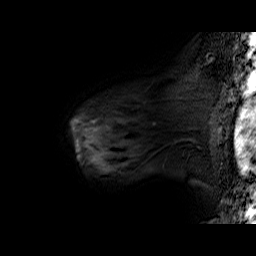
Breast MRI (dynamic contrast-enhanced), one sagittal slice. Slice 49 of 60 in the series (ordered by position). Dynamic contrast-enhanced series, time point 2 of 6 at this slice position (early post-contrast). 1.5 T. TE 6.4 ms, TR 32.9 ms. 4 mm slice thickness. 256 × 256 image matrix, field of view 200 × 200 mm. Female patient. Case-level facts recorded for this patient, not image findings: setting: breast cancer imaged before/during neoadjuvant chemotherapy; receptor status: HER2-positive.
Annotated regions visible in this slice (semi-automatic segmentation, software-assisted and operator-edited):
- analysis volume of interest (the breast-tissue region the enhancement analysis was run in; not a lesion): box from (x=71, y=78) to (x=196, y=160) px
- tumour enhancement mask (voxels above the 100 % enhancement threshold inside the analysis volume of interest): (x=71, y=120)–(x=78, y=130)